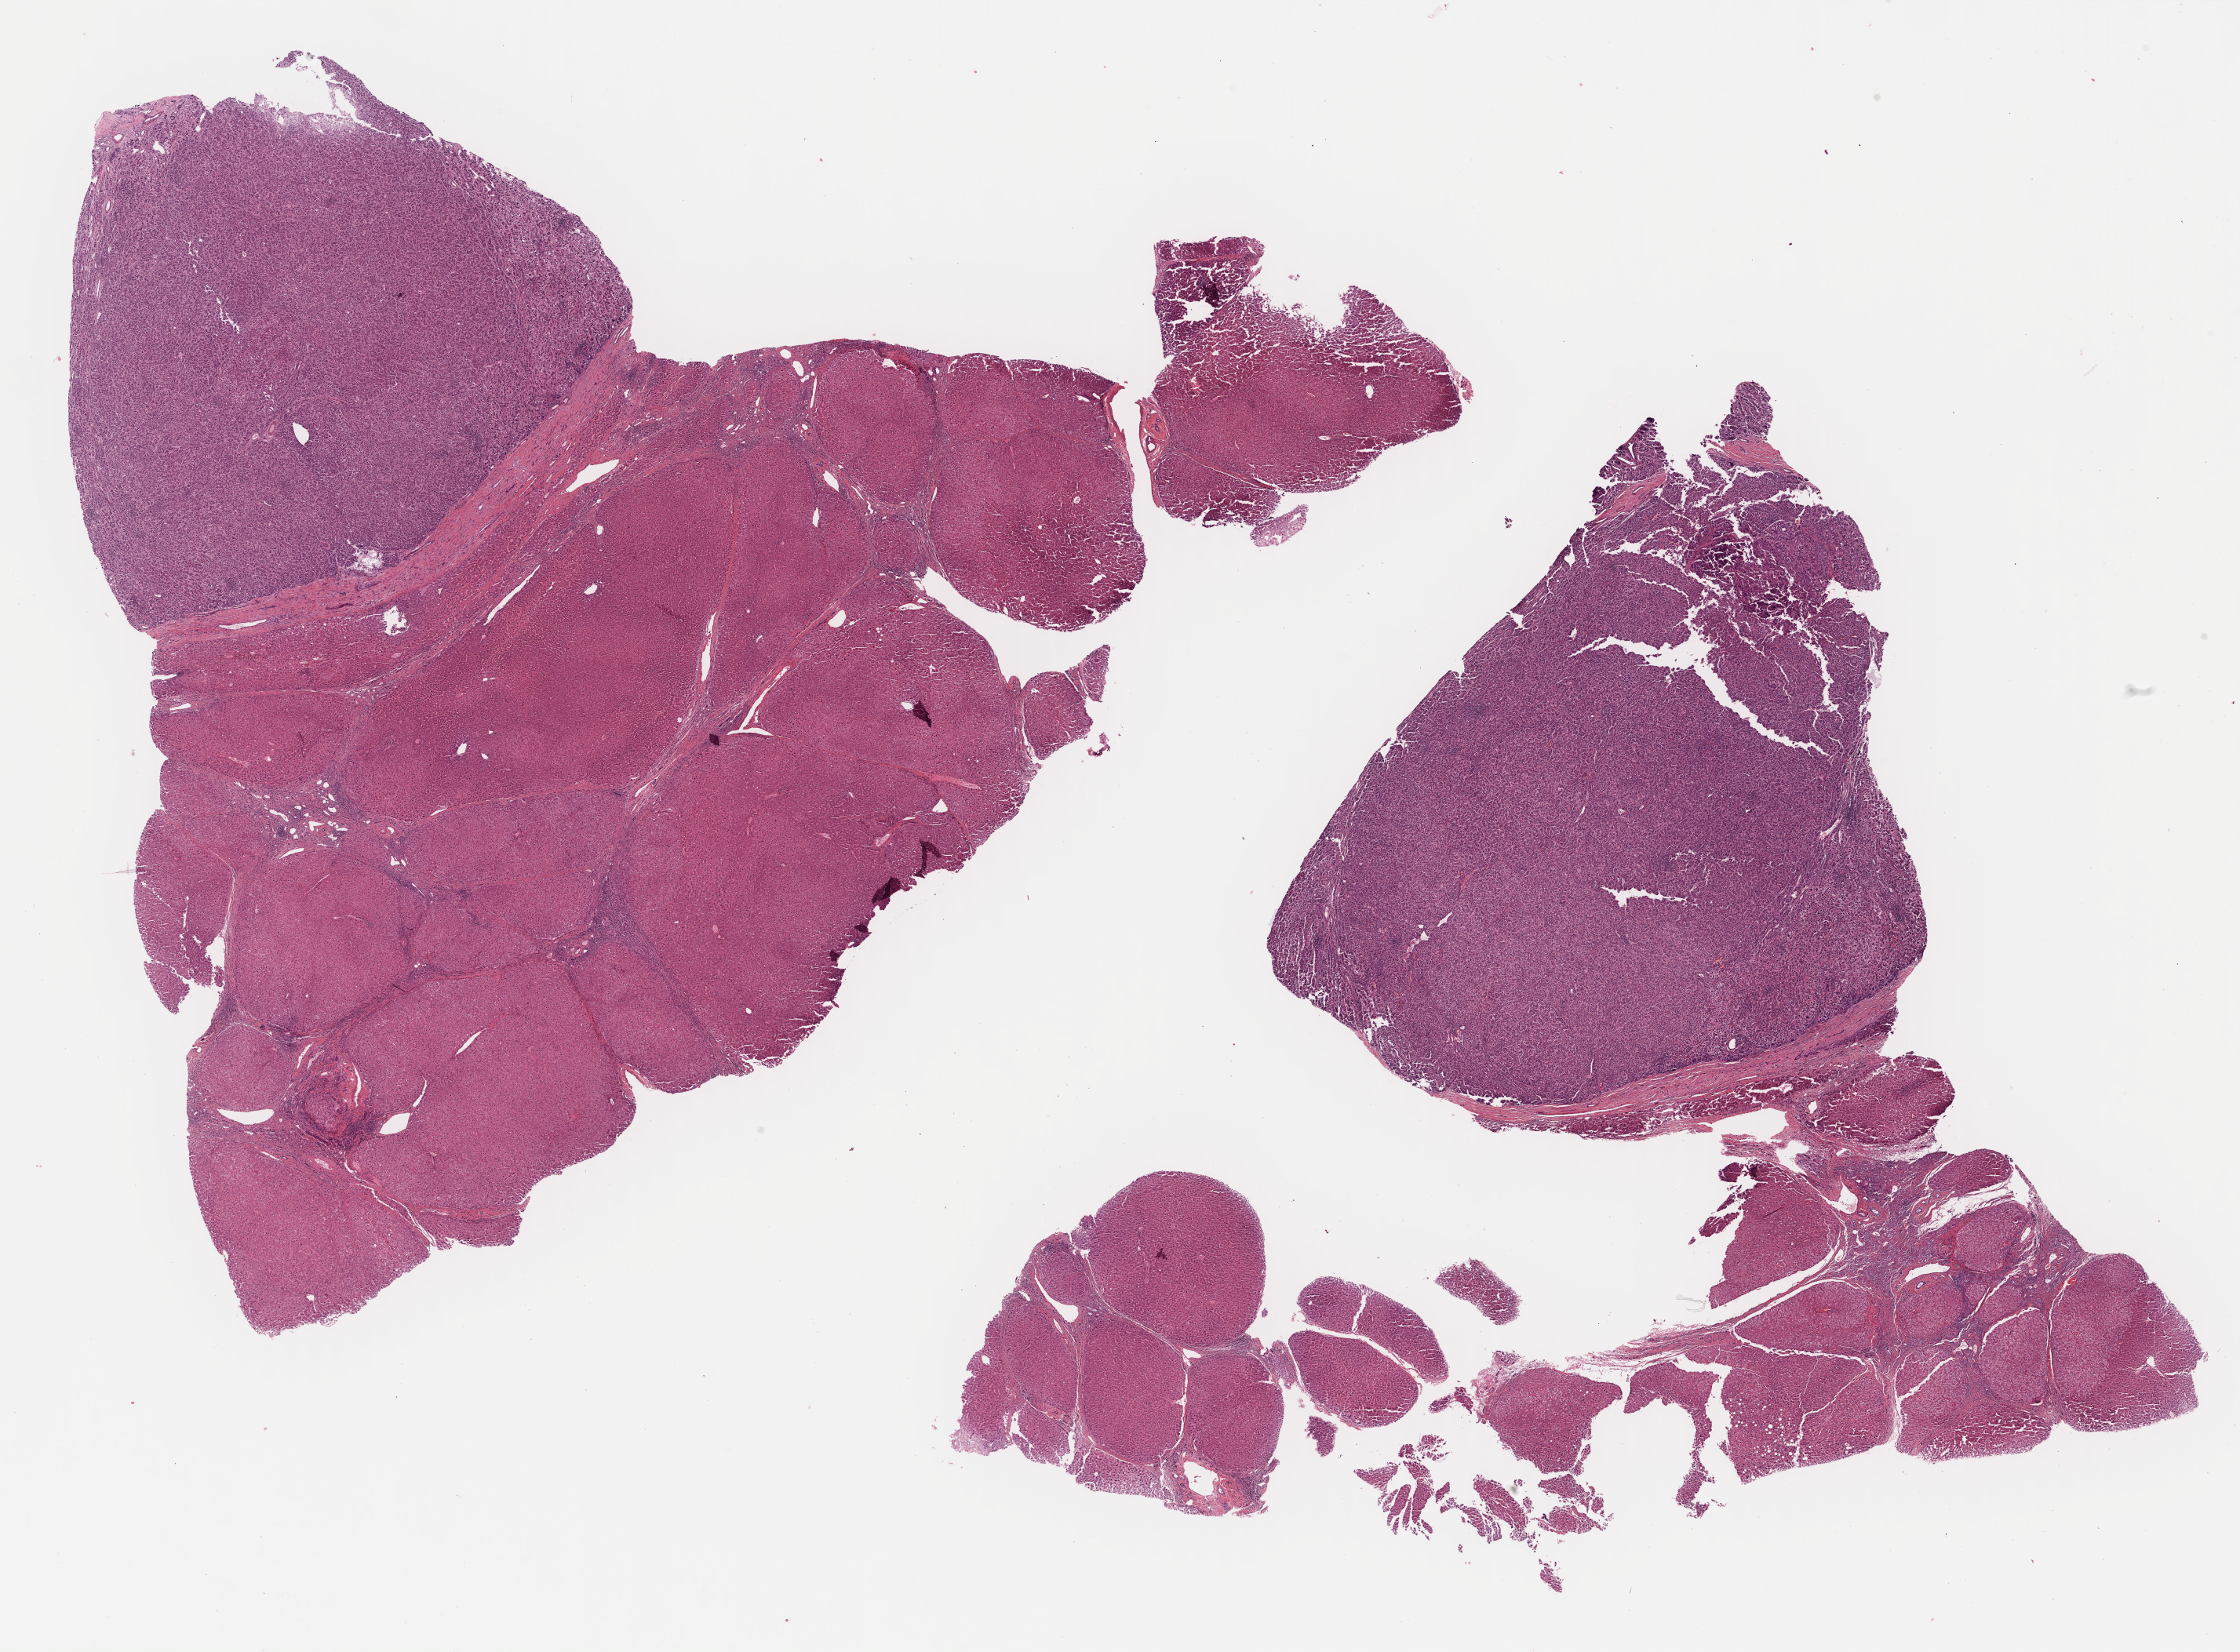
Whole-slide histology image, Hematoxylin and eosin (H&E) stained — low-resolution overview of the scanned area, about 23.1 x 17.0 mm (slide scanned at 40x), formalin-fixed paraffin-embedded (FFPE) diagnostic section, primary tumour sample from the liver. Male, age 46 years at initial diagnosis. Histologic grade: G2 (moderately differentiated).
* TNM: T1 N0 M0
* AJCC pathologic stage: I
* histologic diagnosis: Hepatocellular carcinoma, NOS